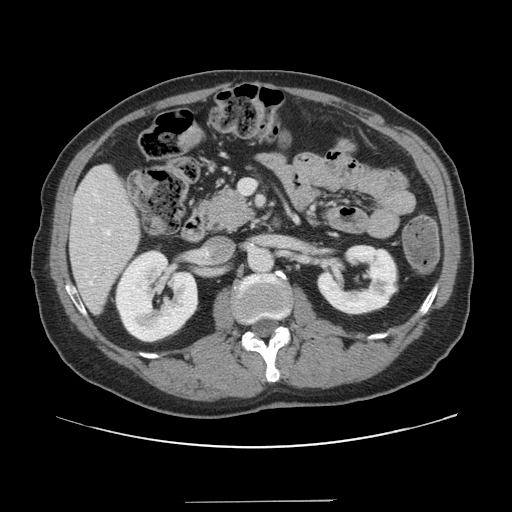
Contrast-enhanced abdominal CT, one axial slice; position 62 of 151 along the scan axis; 120 kVp; intravenous contrast given; soft-tissue window (W 400 / L 40 HU); 512 × 512 image matrix, field of view 399 × 399 mm. Male patient, age 63 years. Case-level facts recorded for this patient, not image findings: diagnosis: colorectal cancer liver metastases, imaged before liver resection.
Structures marked on this image (expert manual segmentation):
- hepatic veins: bounding box (x1, y1, x2, y2) in pixels: (89, 230, 110, 284)
- liver: (72, 166, 140, 313)
- planned liver remnant (the part of the liver to remain after resection): (71, 167, 140, 313)
- portal vein (with intrahepatic branches): (239, 179, 256, 195)